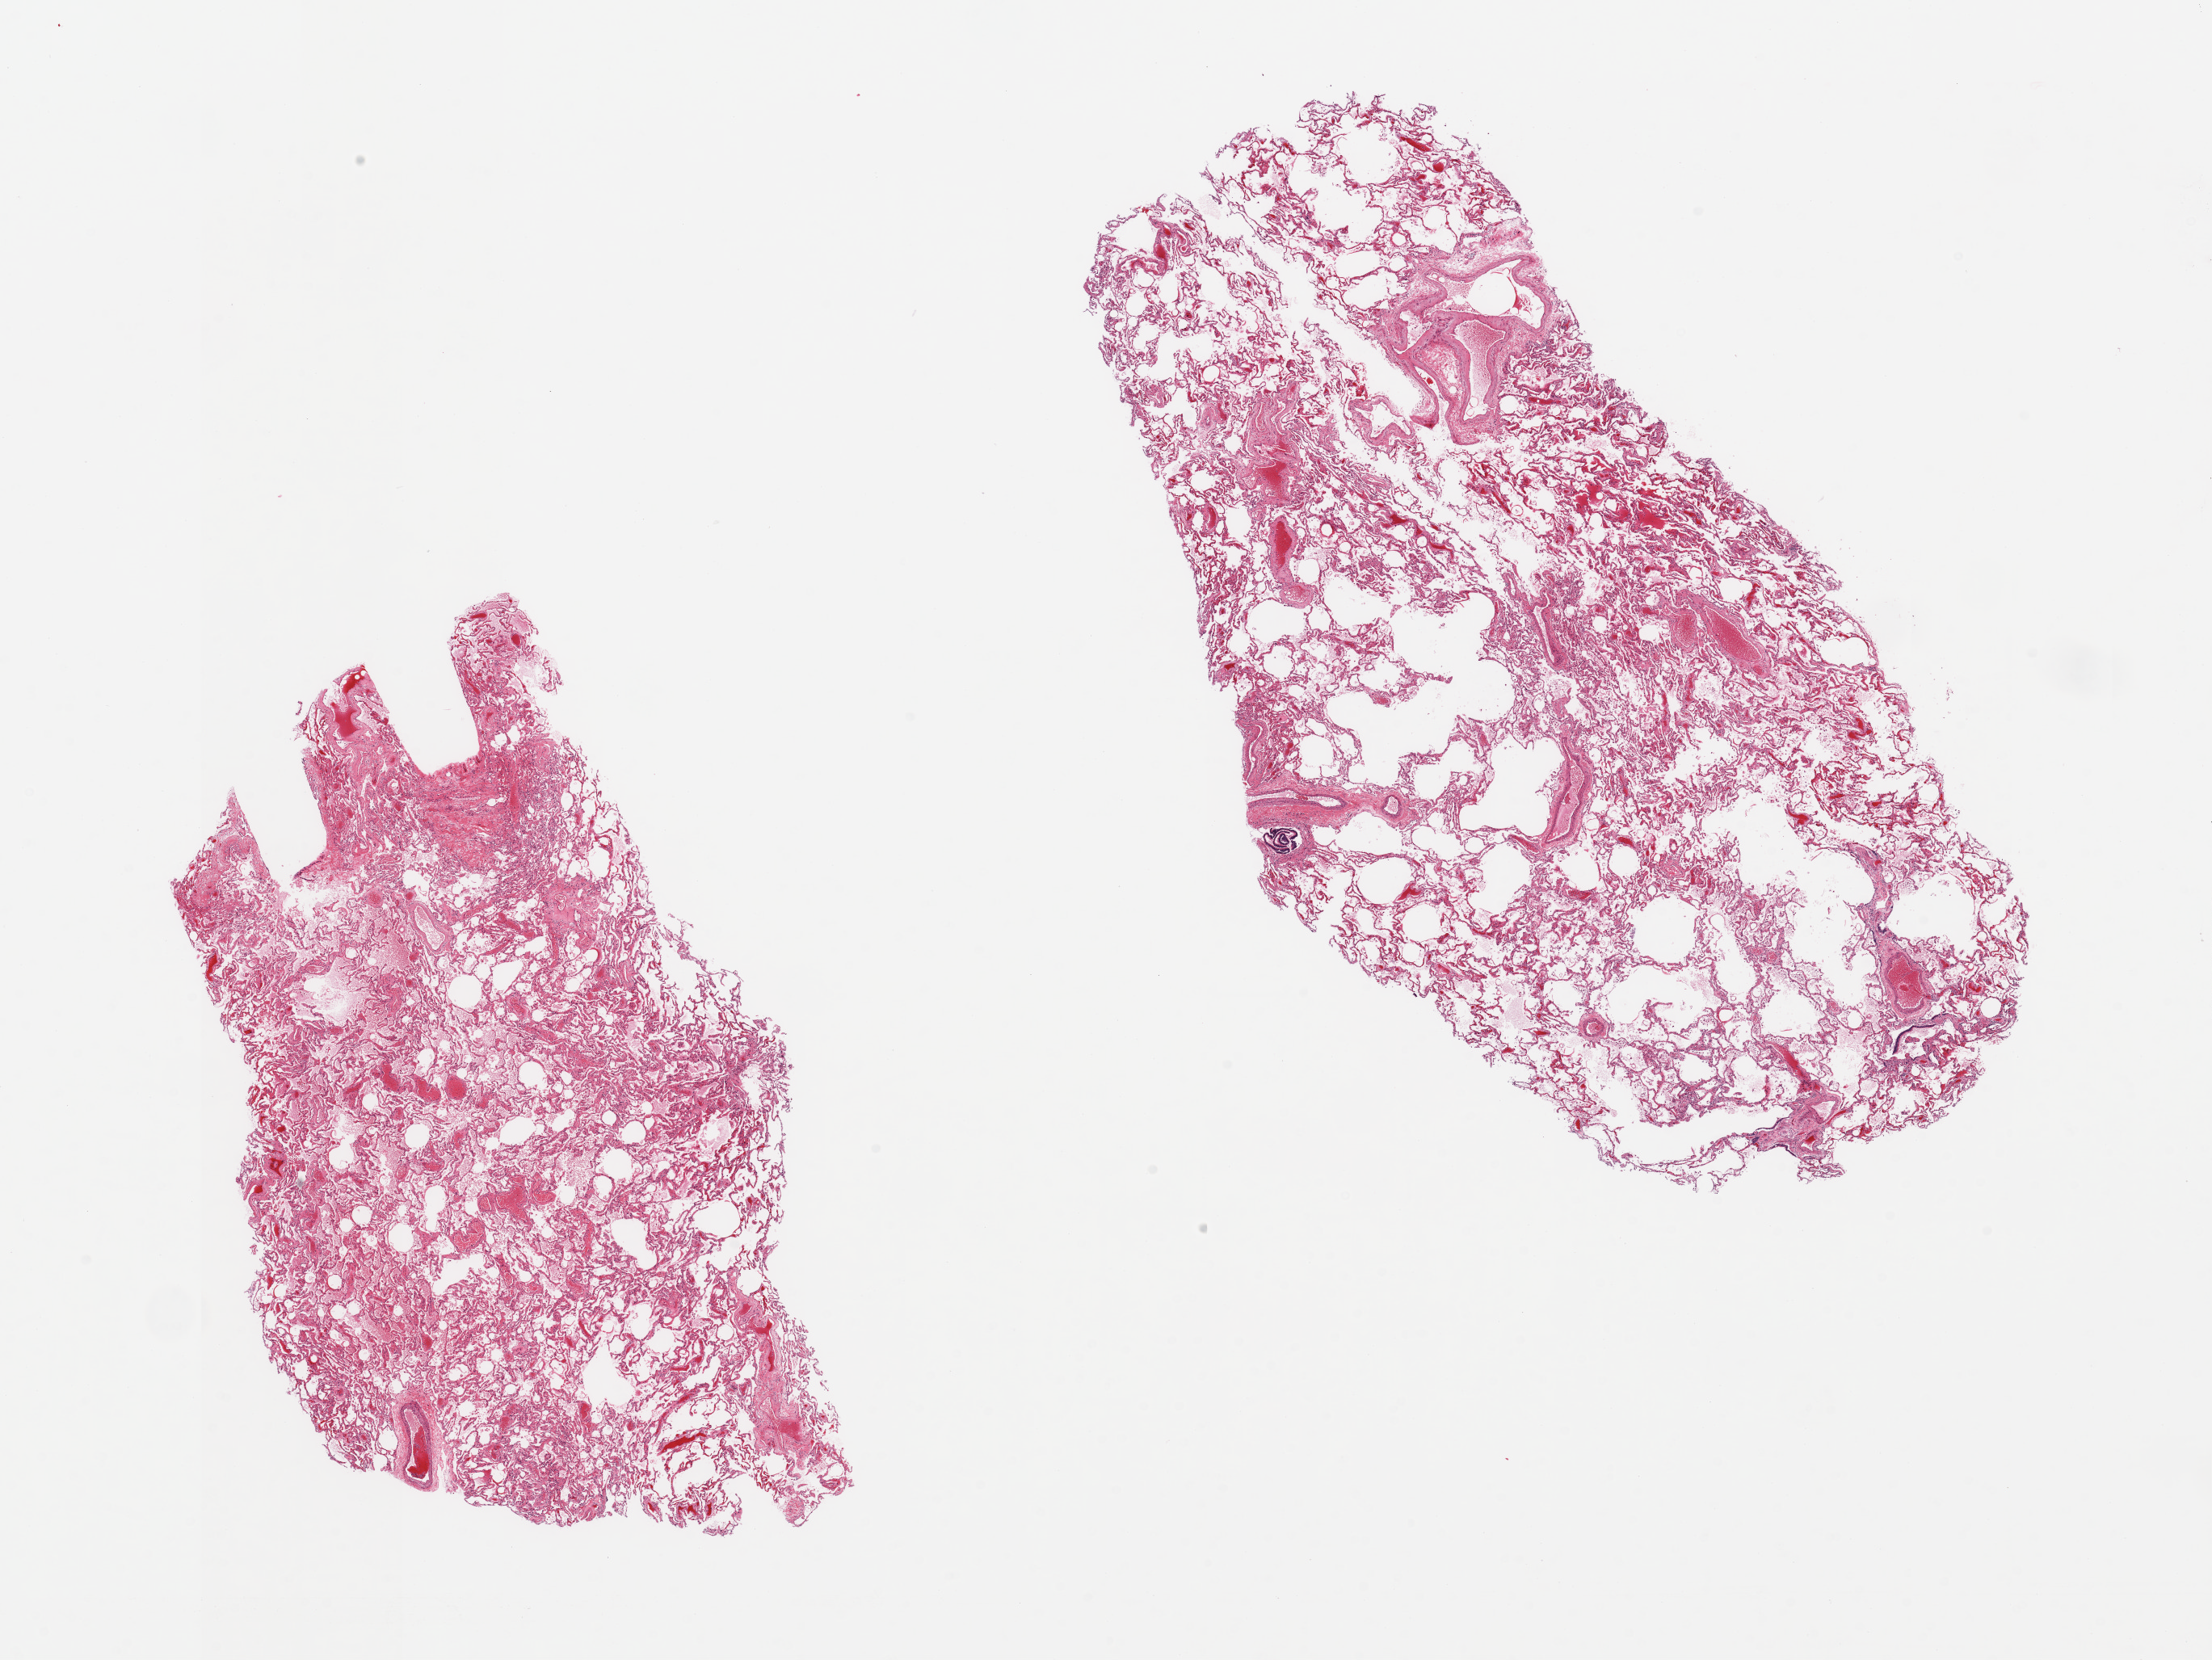
Whole-slide image, hematoxylin and eosin (H&E) stain — whole scanned area (about 21.7 x 16.3 mm, from a 20x scan) shown as a low-resolution overview. PAXgene-fixed, paraffin-embedded tissue. Sampled site (target tissue): lung. Tissue donor sample.
Pathologist's review note for this sample: 2 pieces, moderate edema/congestion.